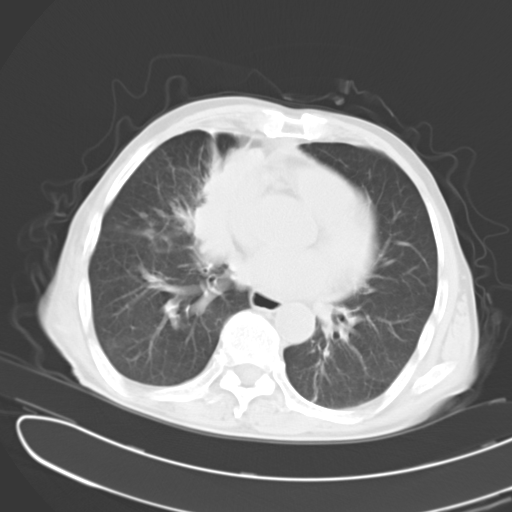
Chest CT, one axial slice. Slice 8 of 24 in the series (ordered by position). Reconstruction kernel B40f. 120 kVp. Lung window (W 1500 / L -600 HU). 10 mm slice thickness. 512 × 512 image matrix. Male patient, age 65 years. From the clinical record (not read from this slice): clinical TNM (as recorded): T2 N3 M1; histopathological grade: G3.
Annotated regions visible in this slice (rectangle marked by the reading radiologist):
- lung tumour (recorded histology: small cell carcinoma): bounding box [x1, y1, x2, y2] px = [187, 127, 266, 255]